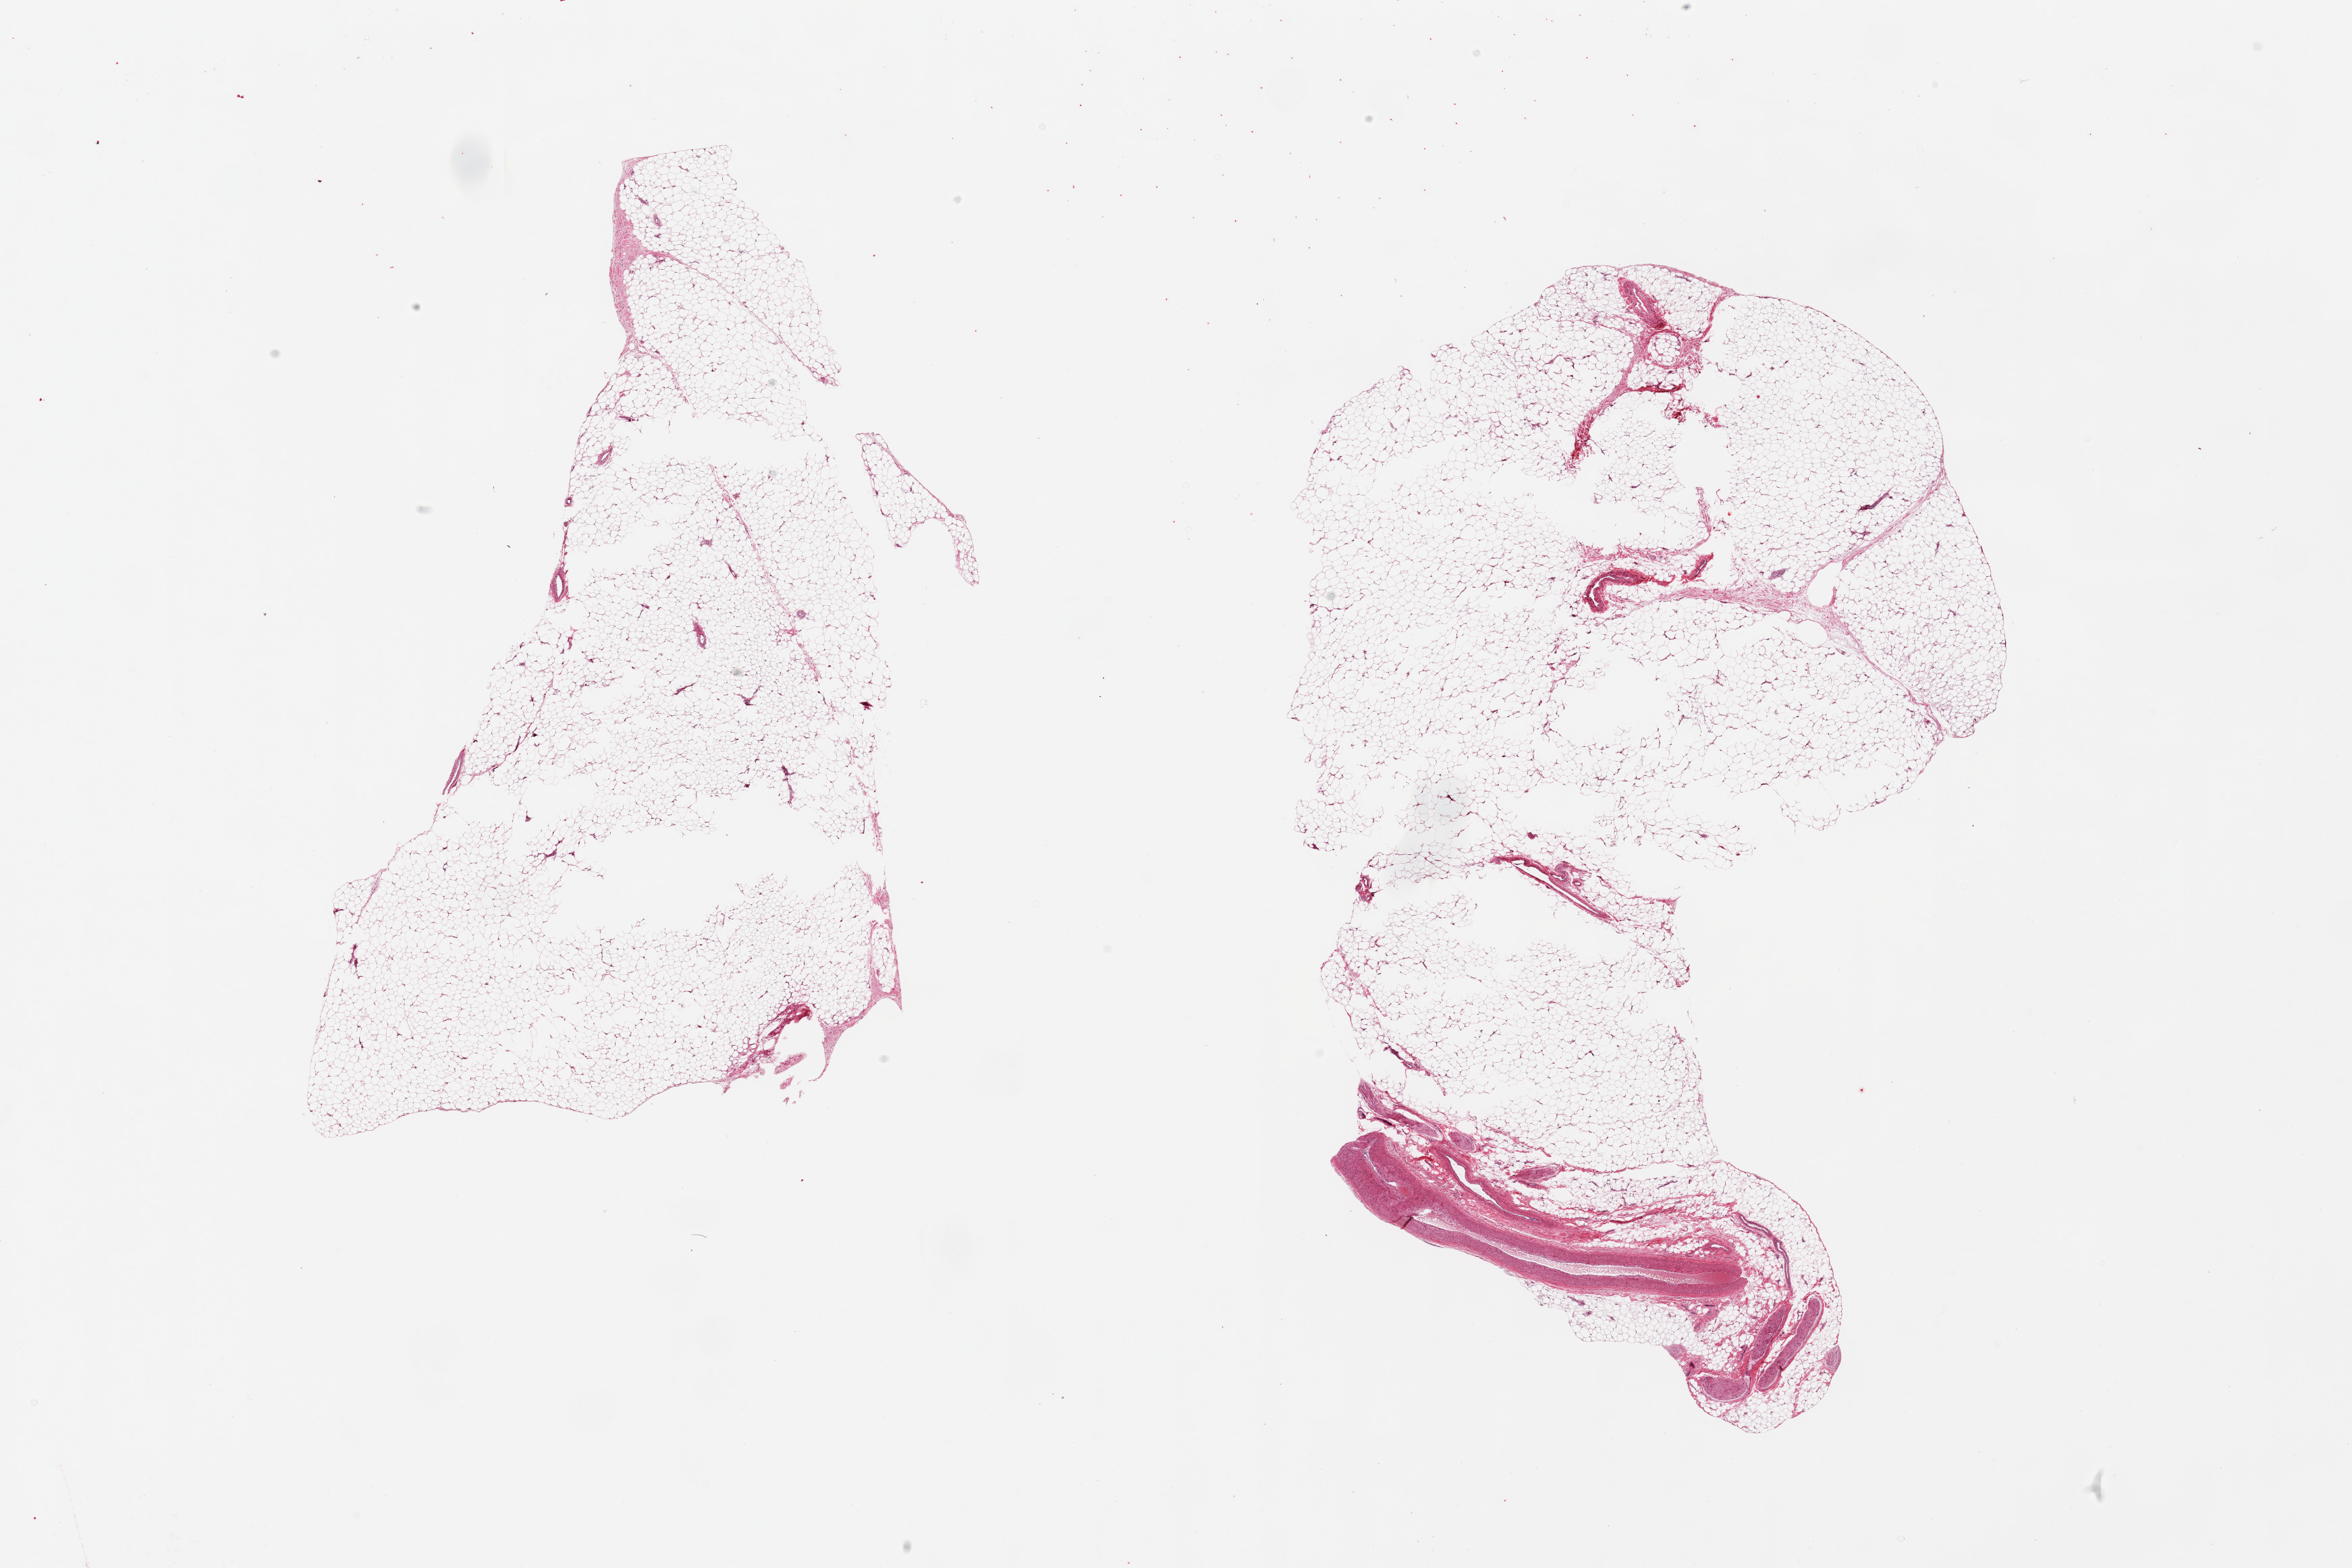
Haematoxylin and eosin whole-slide image, brightfield, whole scanned area (about 27.6 x 18.4 mm) shown as a low-resolution overview. PAXgene-fixed, paraffin-embedded tissue. Target tissue: adipose tissue. Donor tissue sample. Female donor.
* review note (as recorded): 2 pieces; prominent artery and nerves at edge of one piece; internal holes